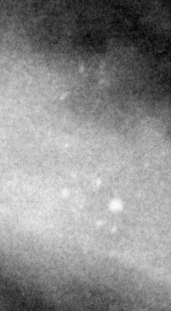
Cropped region of a digitized screen-film mammogram centred on a radiologist-marked abnormality; right breast; MLO view; BI-RADS breast density category 4 (scale 1–4).
Finding: calcifications, morphology pleomorphic, distribution clustered; BI-RADS assessment category 4; pathology (as recorded): malignant.